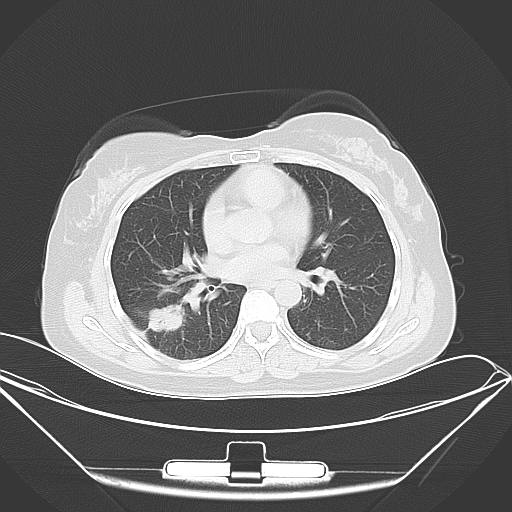
Chest CT, one axial slice. Slice 20 of 46 in the series (ordered by position). 120 kVp. Lung window (W 1500 / L -600 HU). 5 mm slice thickness. 512 × 512 image matrix, field of view 407 × 407 mm. Female patient, age 42 years. From the clinical record (not read from this slice): clinical TNM (as recorded): T1c N0 M1a.
Annotated regions visible in this slice (bounding box drawn by a radiologist):
- lung tumour (recorded histology: adenocarcinoma): bounding box (x1, y1, x2, y2) in pixels: (143, 302, 188, 337)